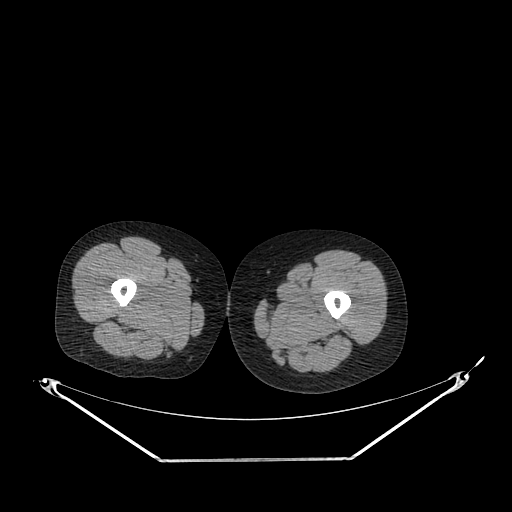
CT of an extremity soft-tissue mass (from a PET/CT study), one axial slice. Reconstruction kernel SOFT. 120 kVp. Soft-tissue window (W 400 / L 40 HU). 3.75 mm slice thickness. 512 × 512 image matrix. Female patient. Case-level facts recorded for this patient, not image findings: histological type: pleiomorphic leiomyosarcoma; grade: intermediate; site of the primary tumour: left thigh.
Outlined on this slice (expert contour drawn on MRI and transferred to this co-registered scan by the dataset authors):
- gross tumour volume including surrounding oedema: bounding box [x1, y1, x2, y2] px = [315, 311, 321, 316]